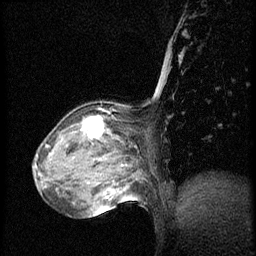
Breast MRI (dynamic contrast-enhanced), one sagittal slice; dynamic contrast-enhanced series, image 2 of 3 at this slice position (ordered by acquisition); 1.5 T; TE 4.2 ms, TR 20.4 ms; 256 × 256 image matrix, field of view 200 × 200 mm. Patient: female, 64 years. From the clinical record (not read from this slice): setting: breast cancer imaged before/during neoadjuvant chemotherapy; receptor status: HR-positive, HER2-negative.
Annotated regions visible in this slice (semi-automatically segmented with operator editing):
- analysis volume of interest (the breast-tissue region the enhancement analysis was run in; not a lesion): bounding box [x1, y1, x2, y2] px = [48, 102, 142, 186]
- tumour enhancement mask (voxels above the 70 % enhancement threshold inside the analysis volume of interest): [81, 116, 105, 138]